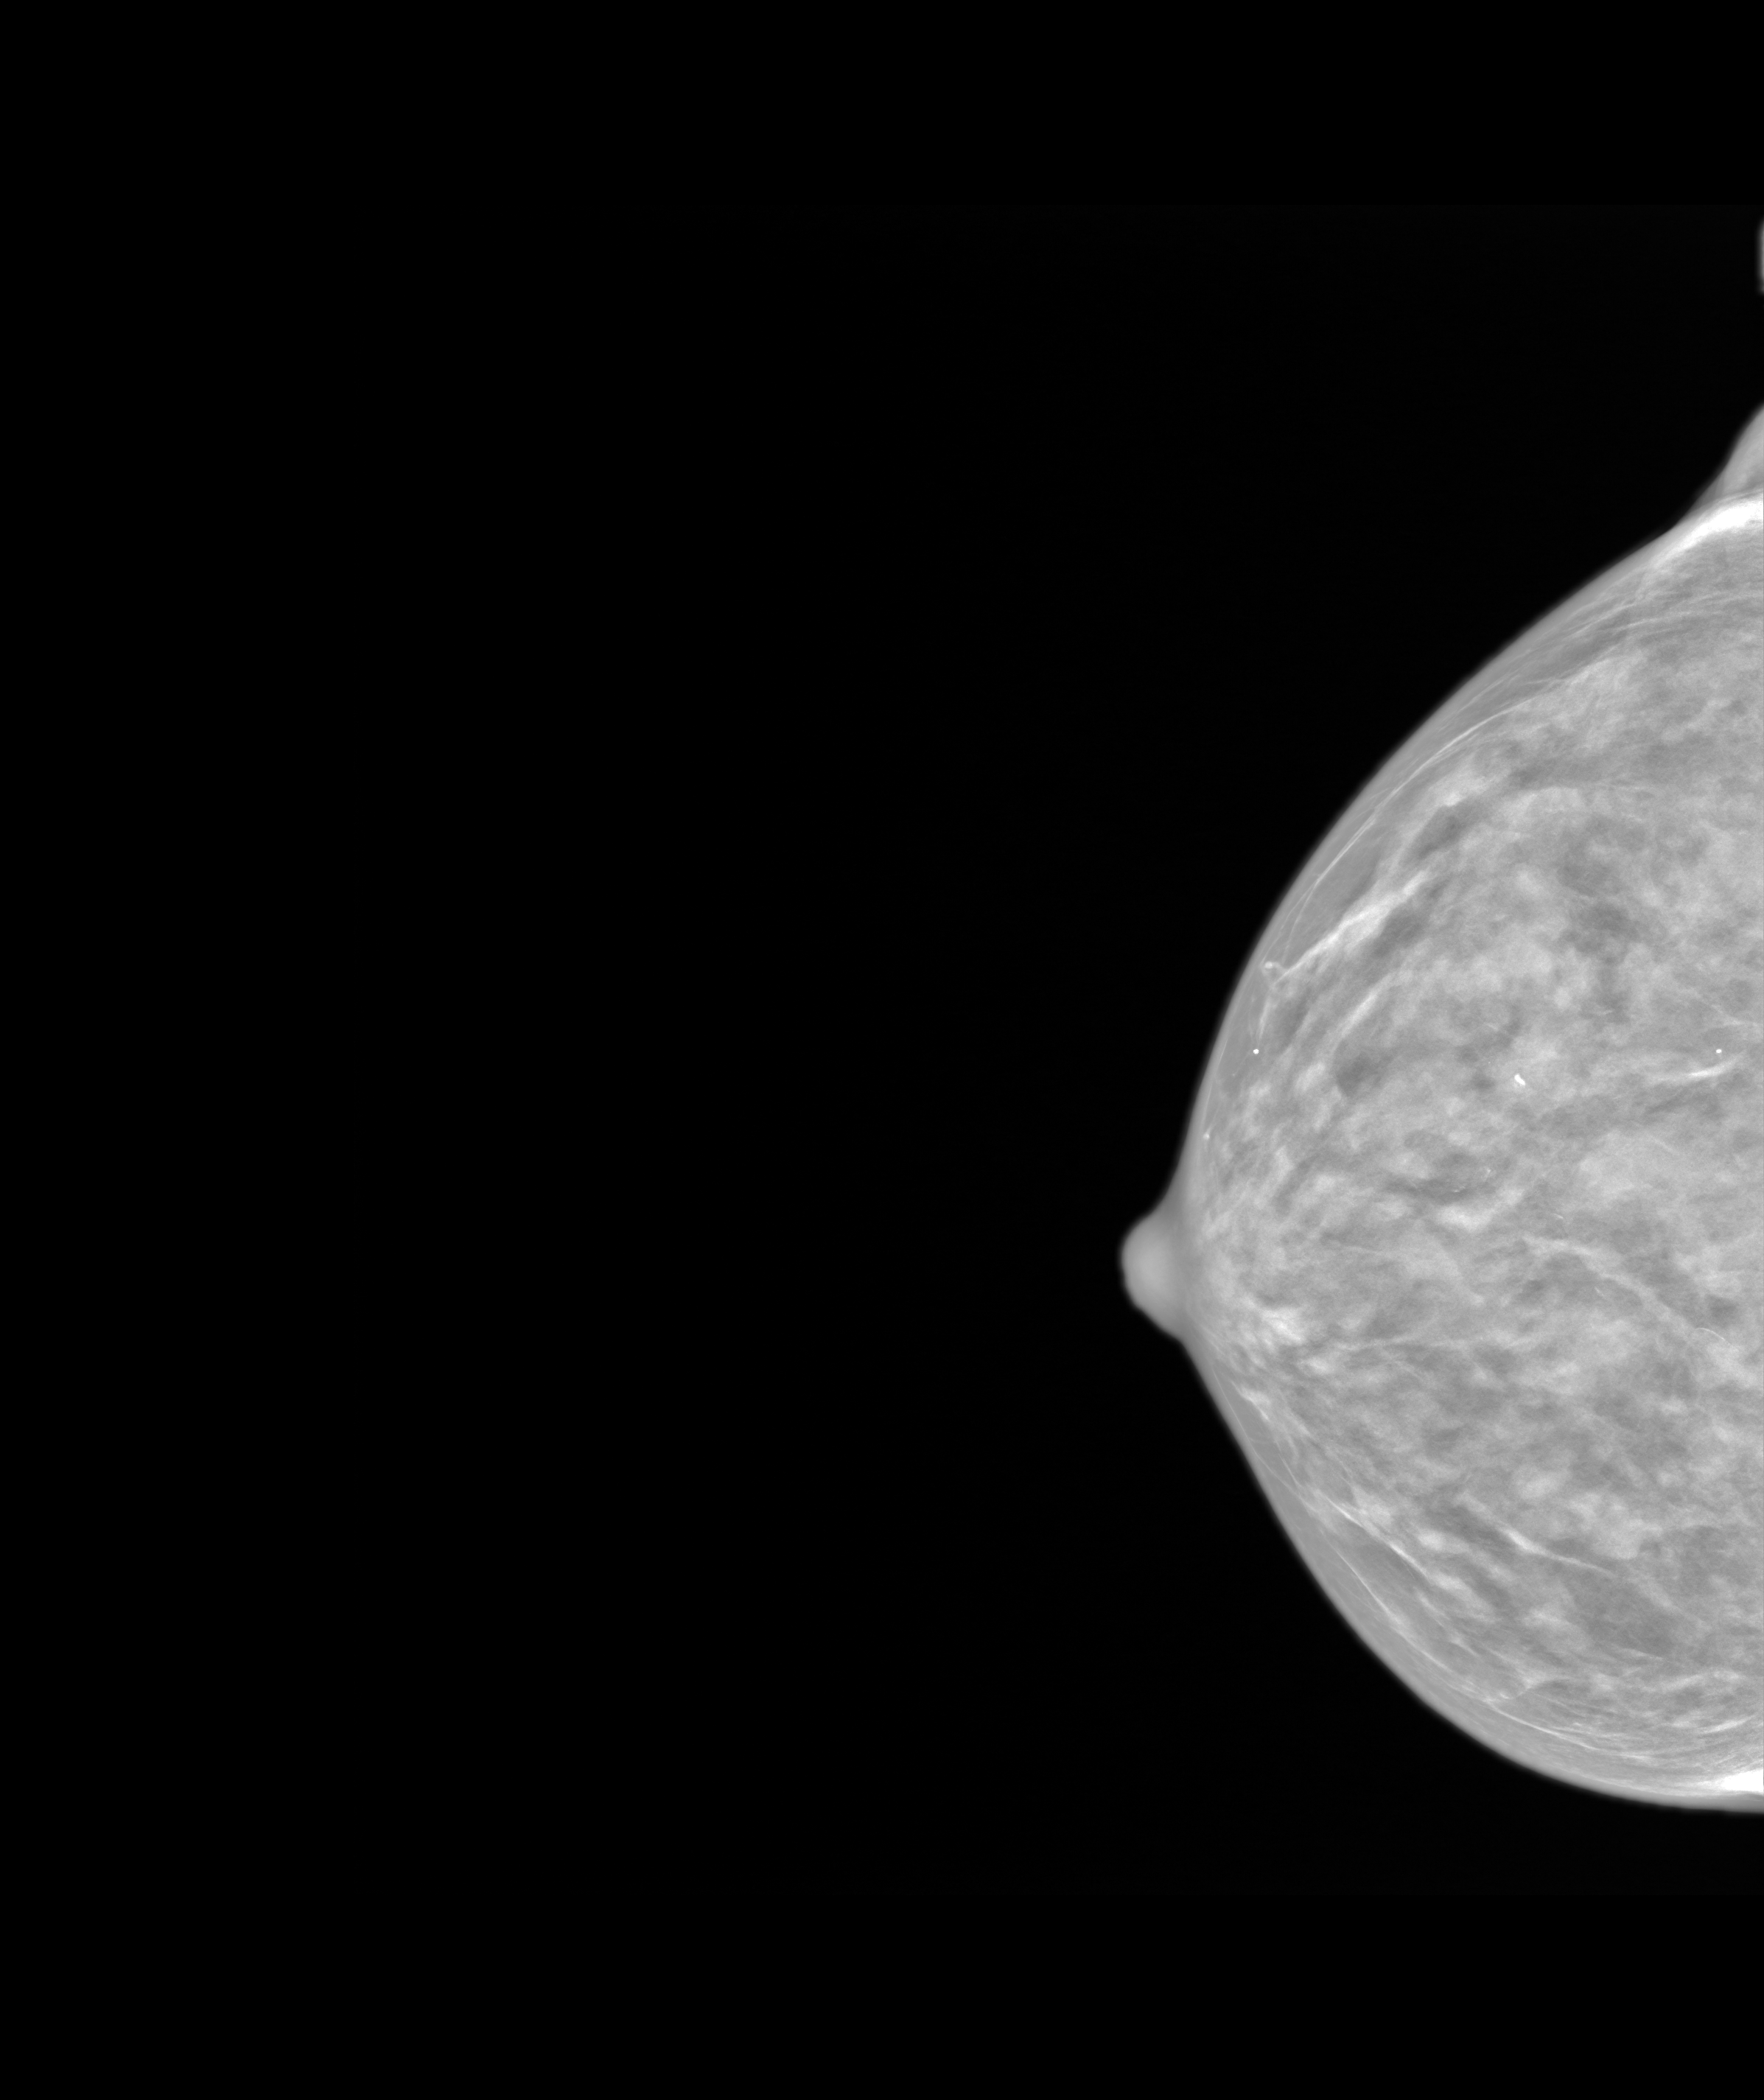
Annual screening mammography examination; system: SenoIris_1SP1.2(425). Patient: female, 74 years.
Image type: synthesized 2-D view from tomosynthesis. Breast: right. Projection: cranio-caudal projection.